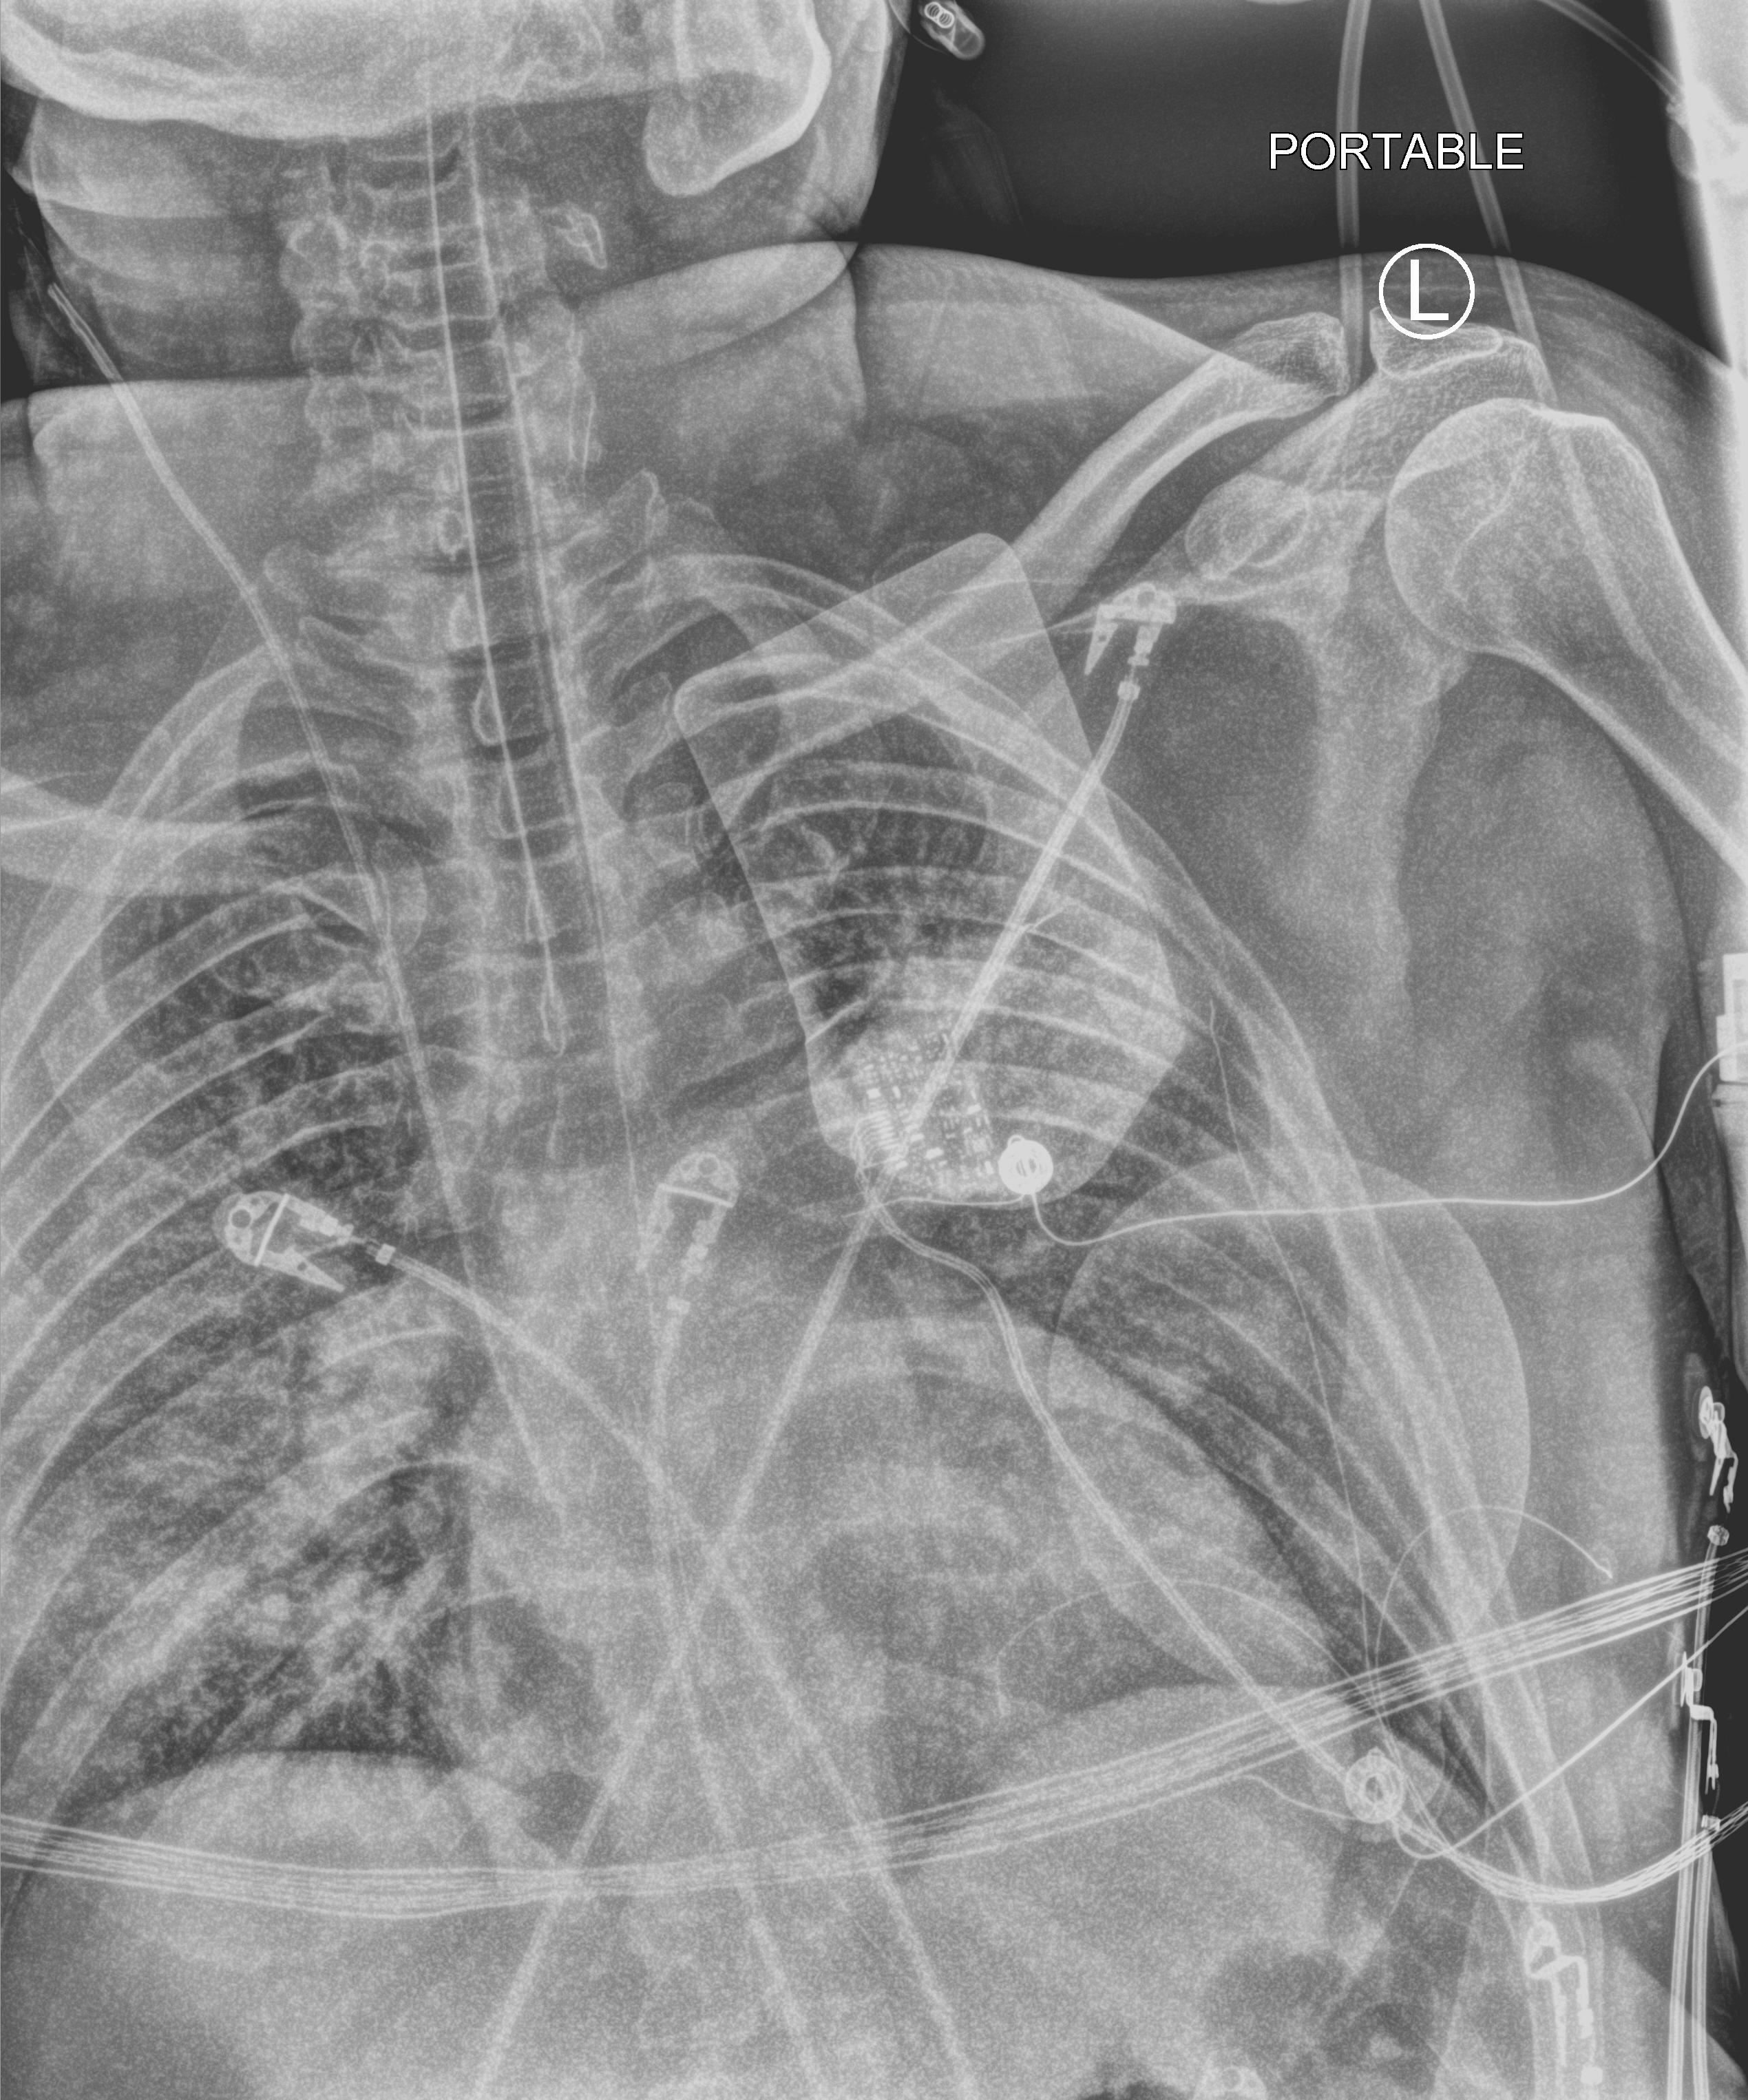
Bedside chest radiograph (computed radiography), anteroposterior (AP) projection. Patient hospitalised with COVID-19; male, aged 18–59 years.
Hospital-stay facts (about this admission, not read from this image; timing relative to this image not recorded):
- smoking status (admission record): never
- length of hospital stay: 75 days
- mechanically ventilated during this hospital stay: yes